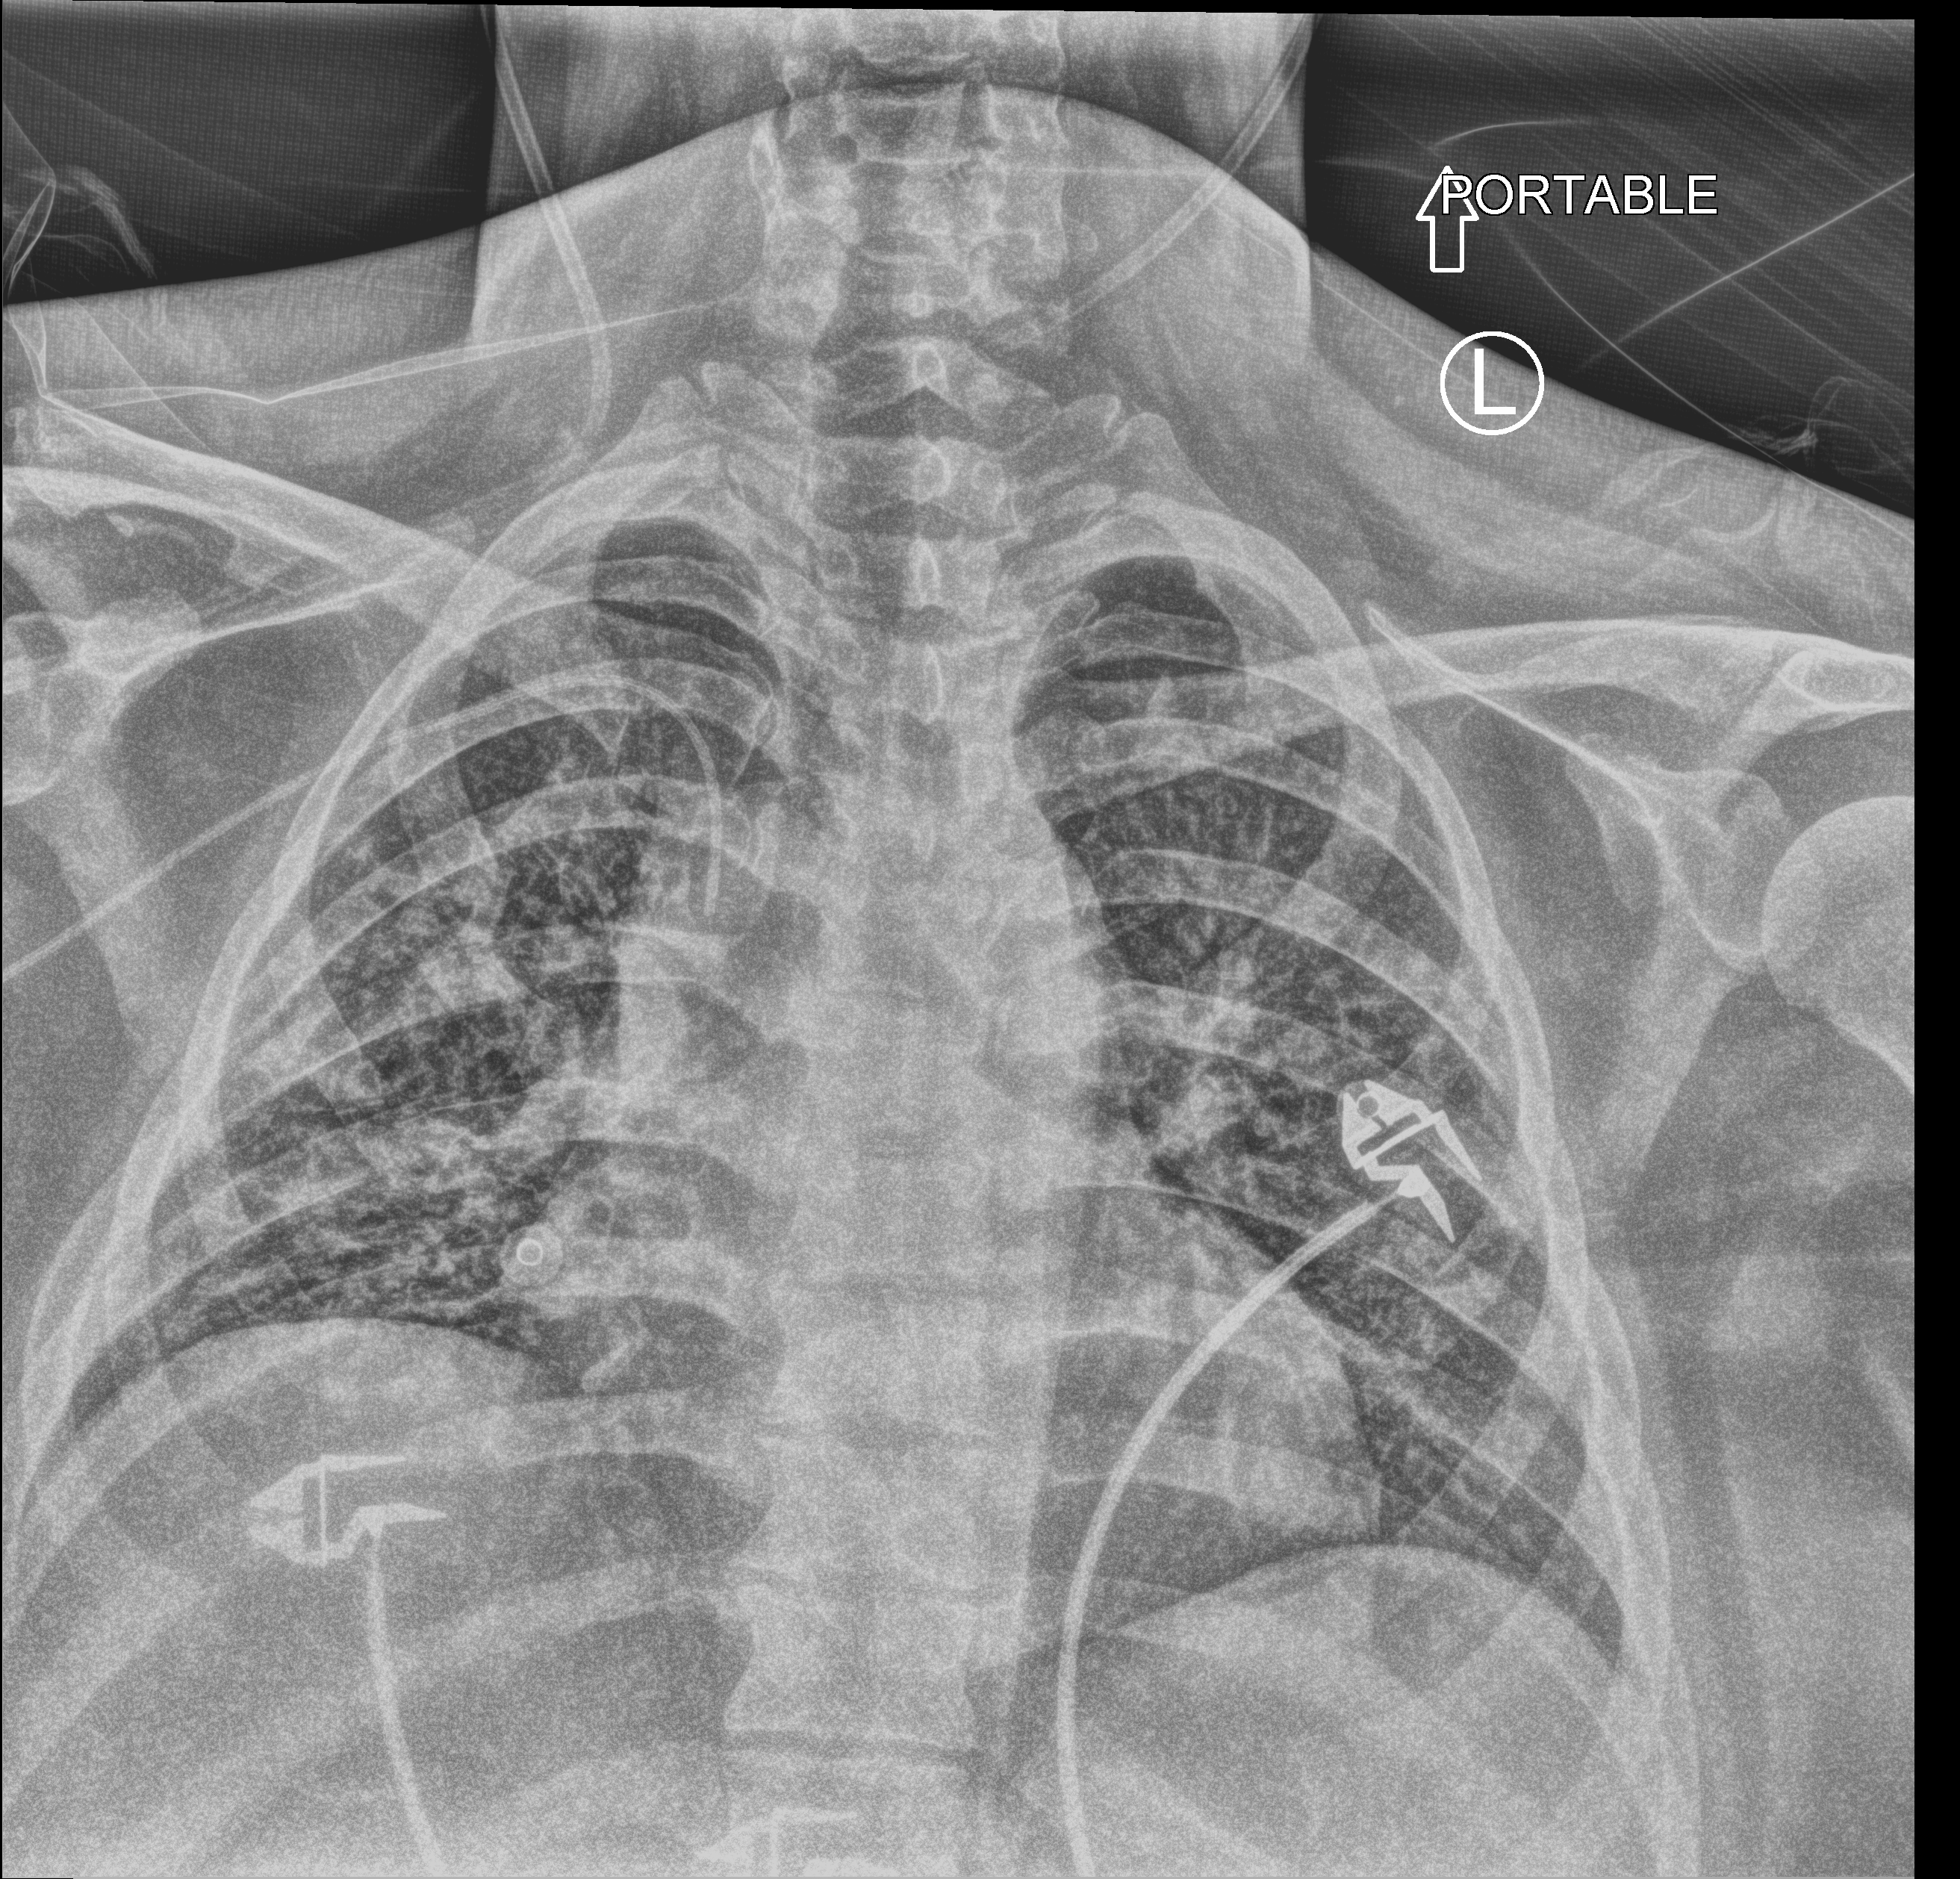
Portable chest radiograph; anteroposterior (AP) projection. Patient hospitalised with COVID-19; female, aged 18–59 years.
Admission-level facts for this patient (not findings on this image; timing relative to this image not recorded): admitted to intensive care during this hospital stay: yes.